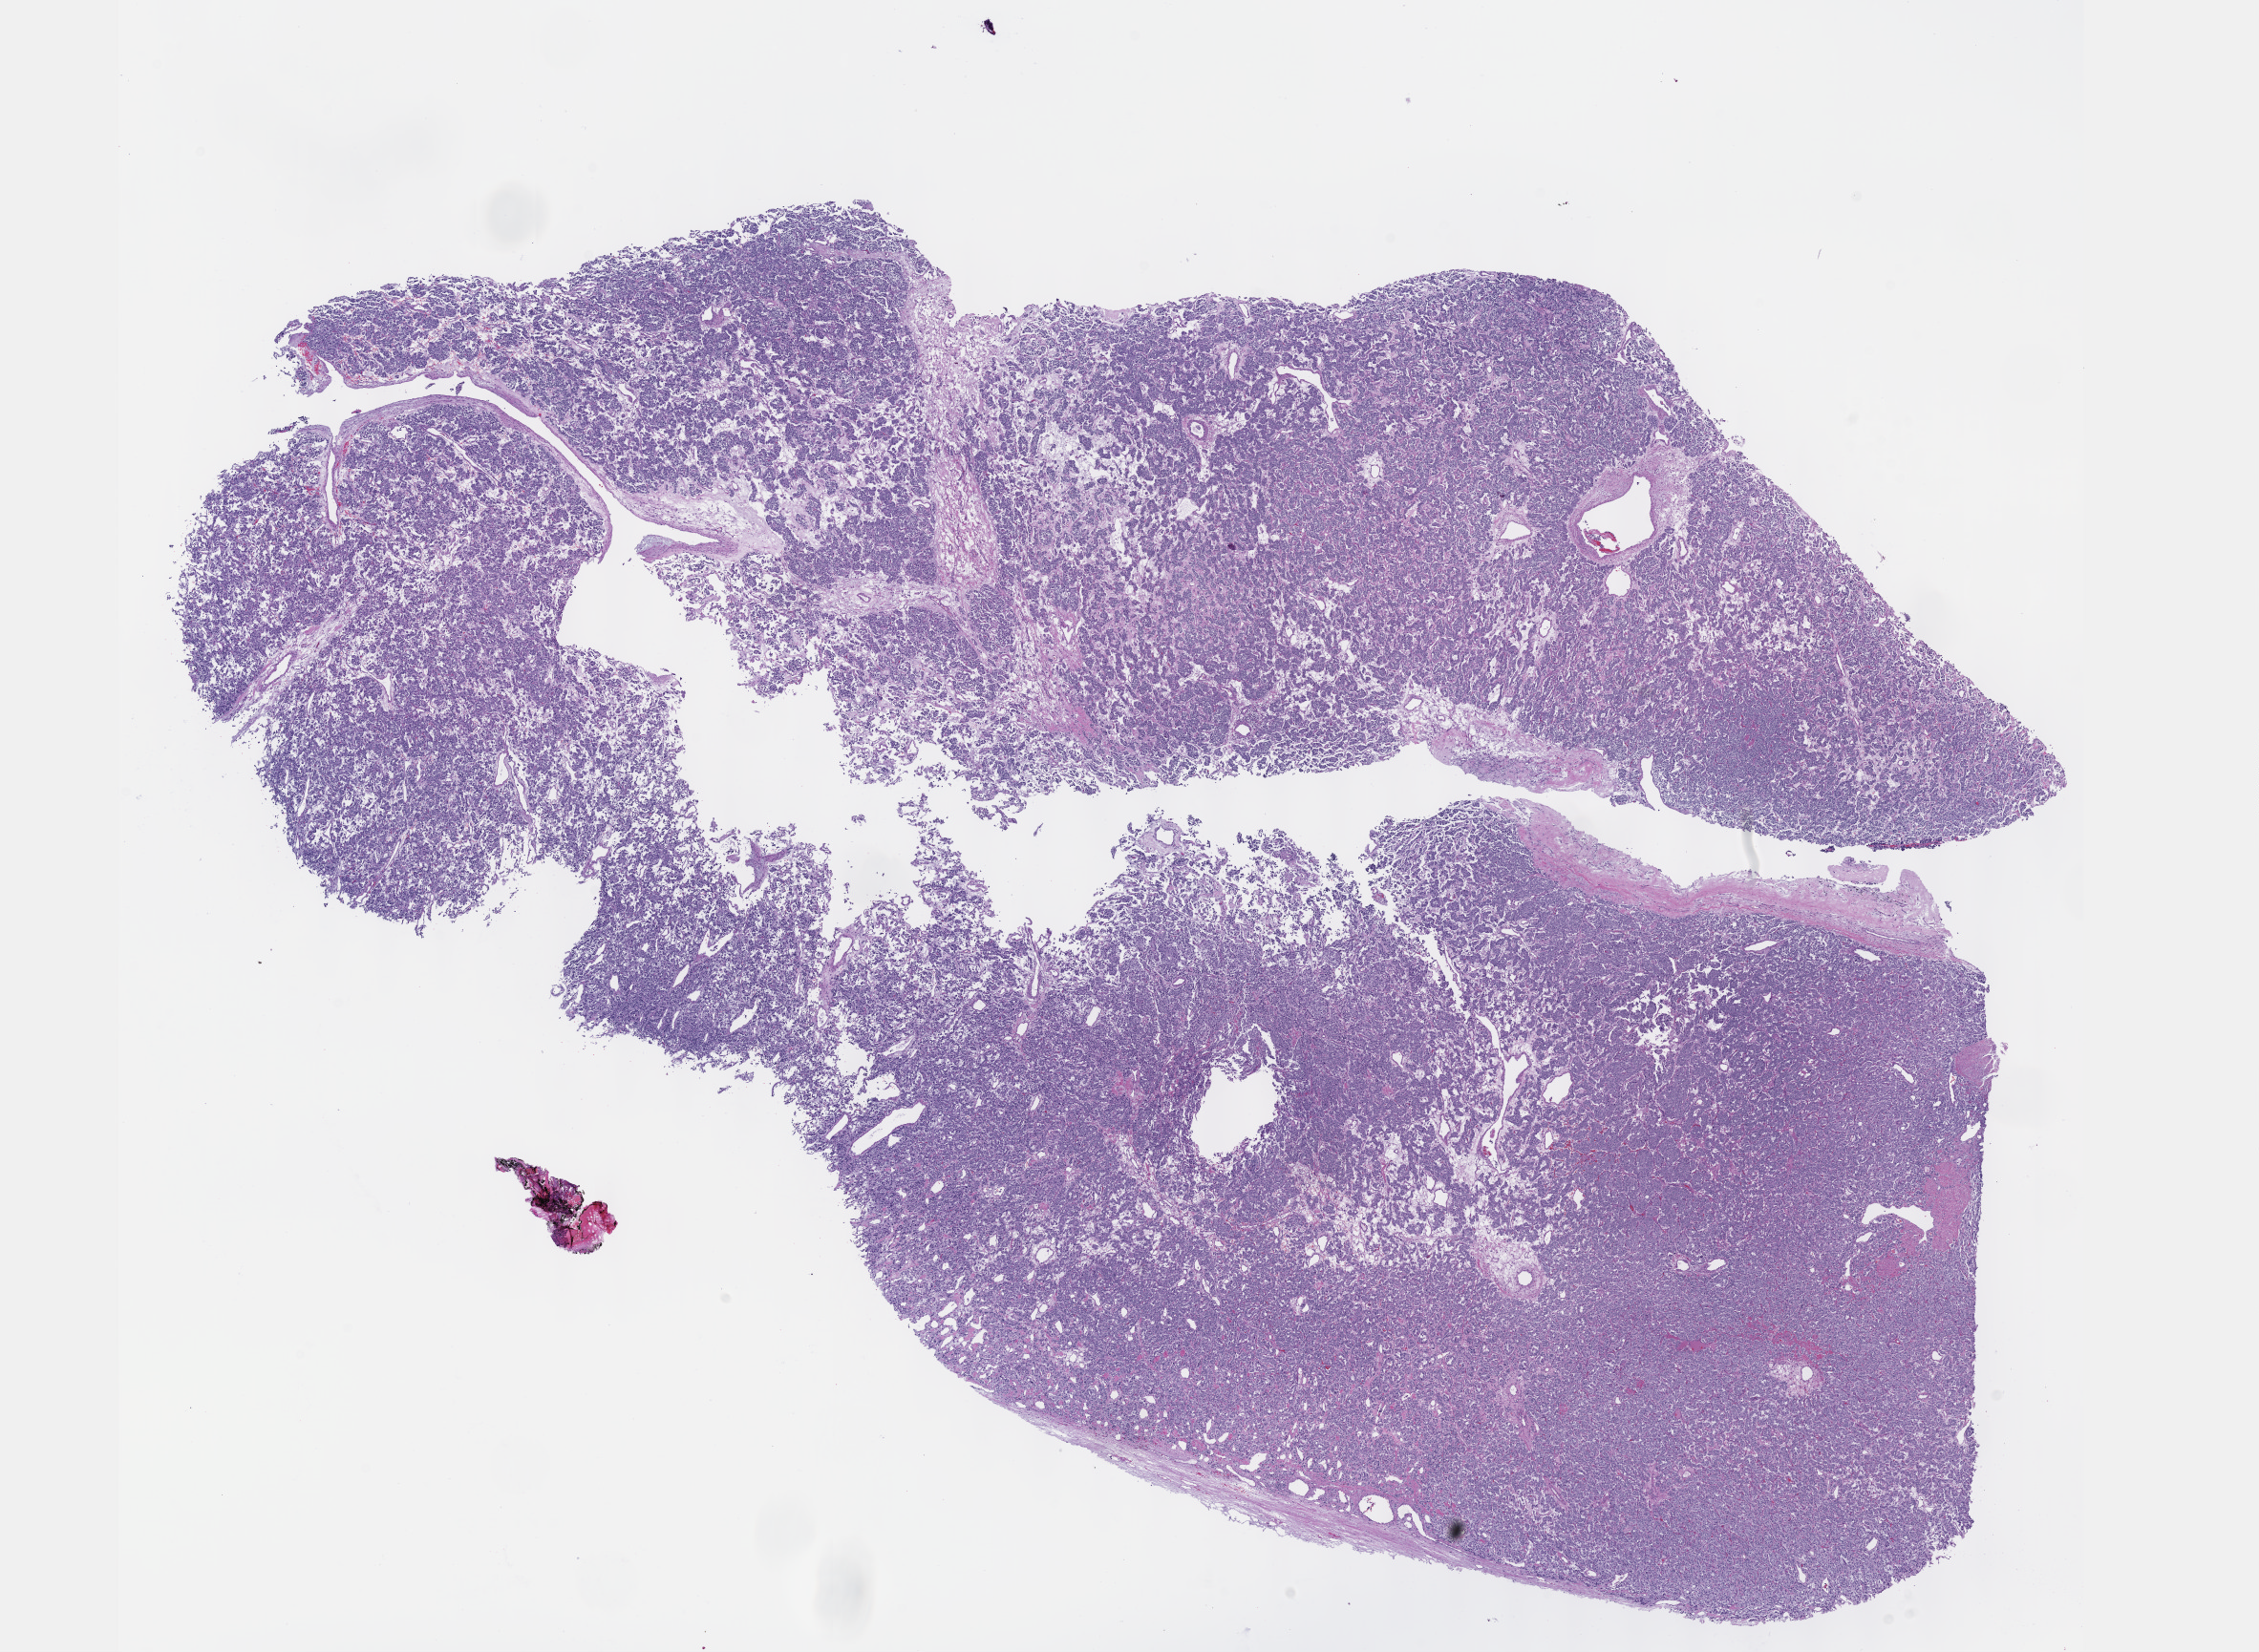
Digitized H&E-stained tissue section (whole slide) — shown as a low-resolution overview of the whole scanned area (about 19.1 x 14.0 mm, from a 40x scan); formalin-fixed paraffin-embedded (FFPE) diagnostic section; primary tumour sample from the adrenal gland. Female patient; age at initial diagnosis 54 years.
Diagnosis: Pheochromocytoma, NOS.